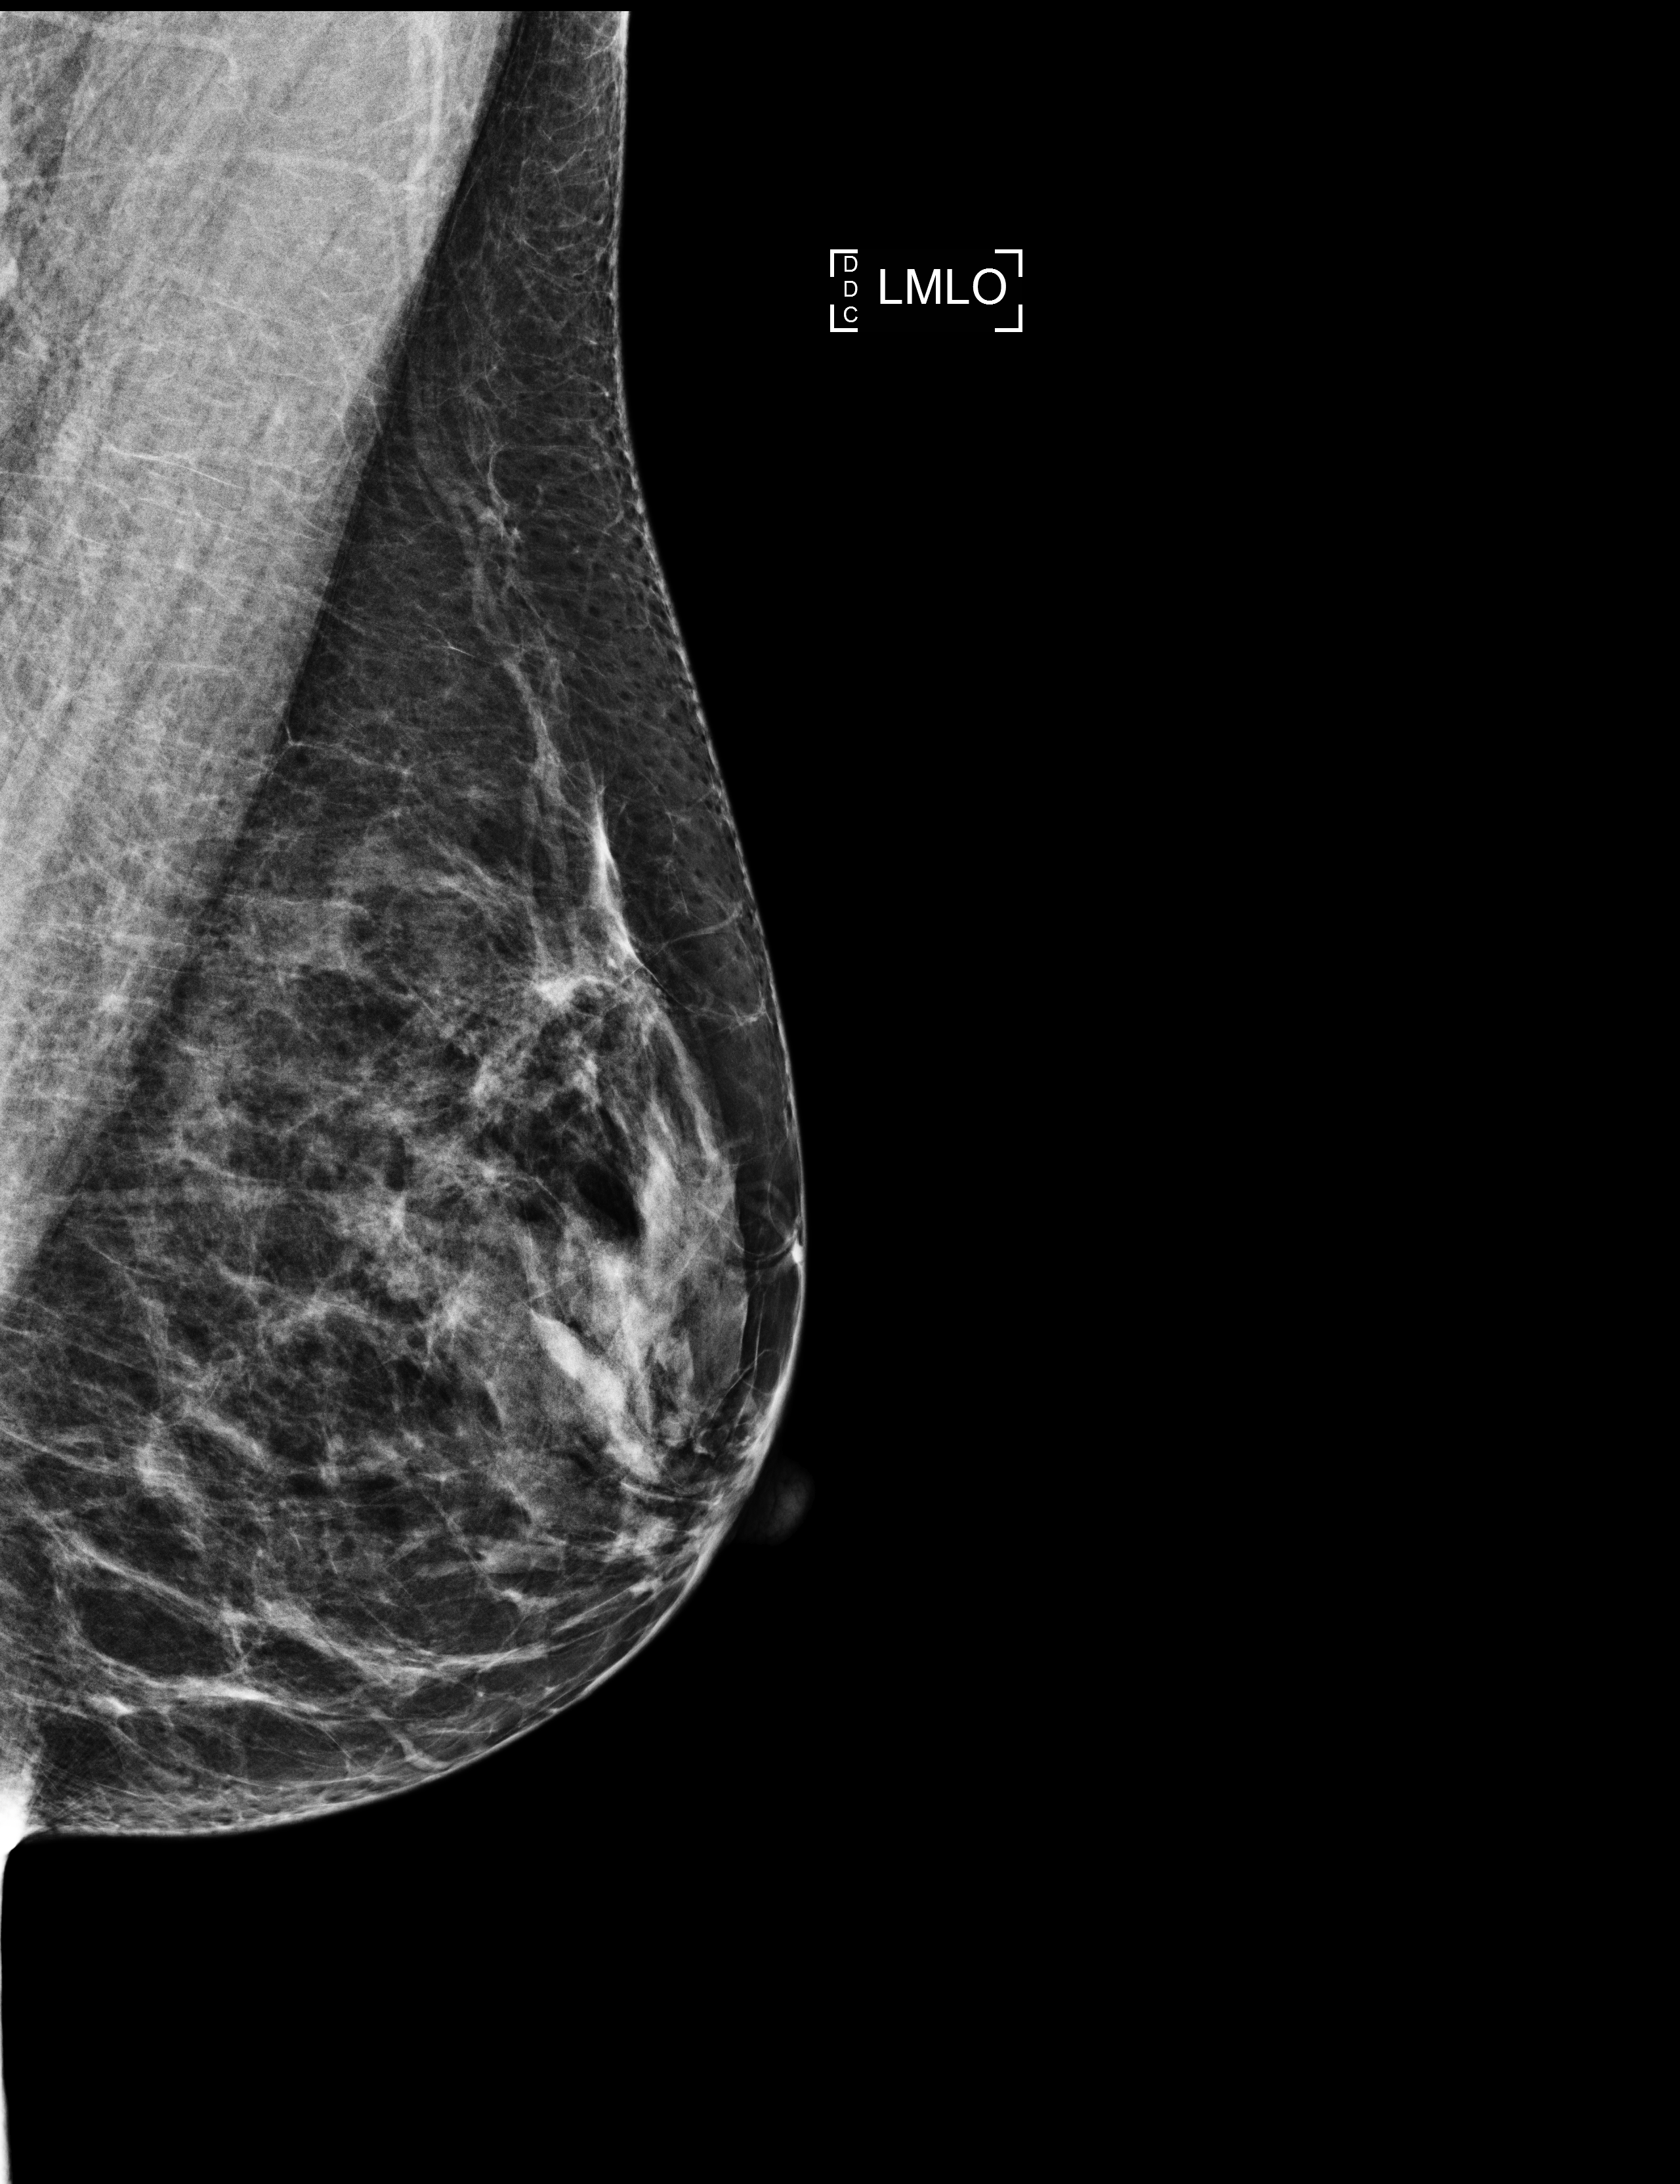
Digital mammogram (FFDM), left breast, MLO view, screening examination, compressed breast thickness 56 mm. Female patient, age 59 years.
- breast density at the screening exam (both breasts): heterogeneously dense (BI-RADS density category c)
- final BI-RADS assessment for this screening round (tomosynthesis exam, both breasts): category 2
- recall: no recall after this screen